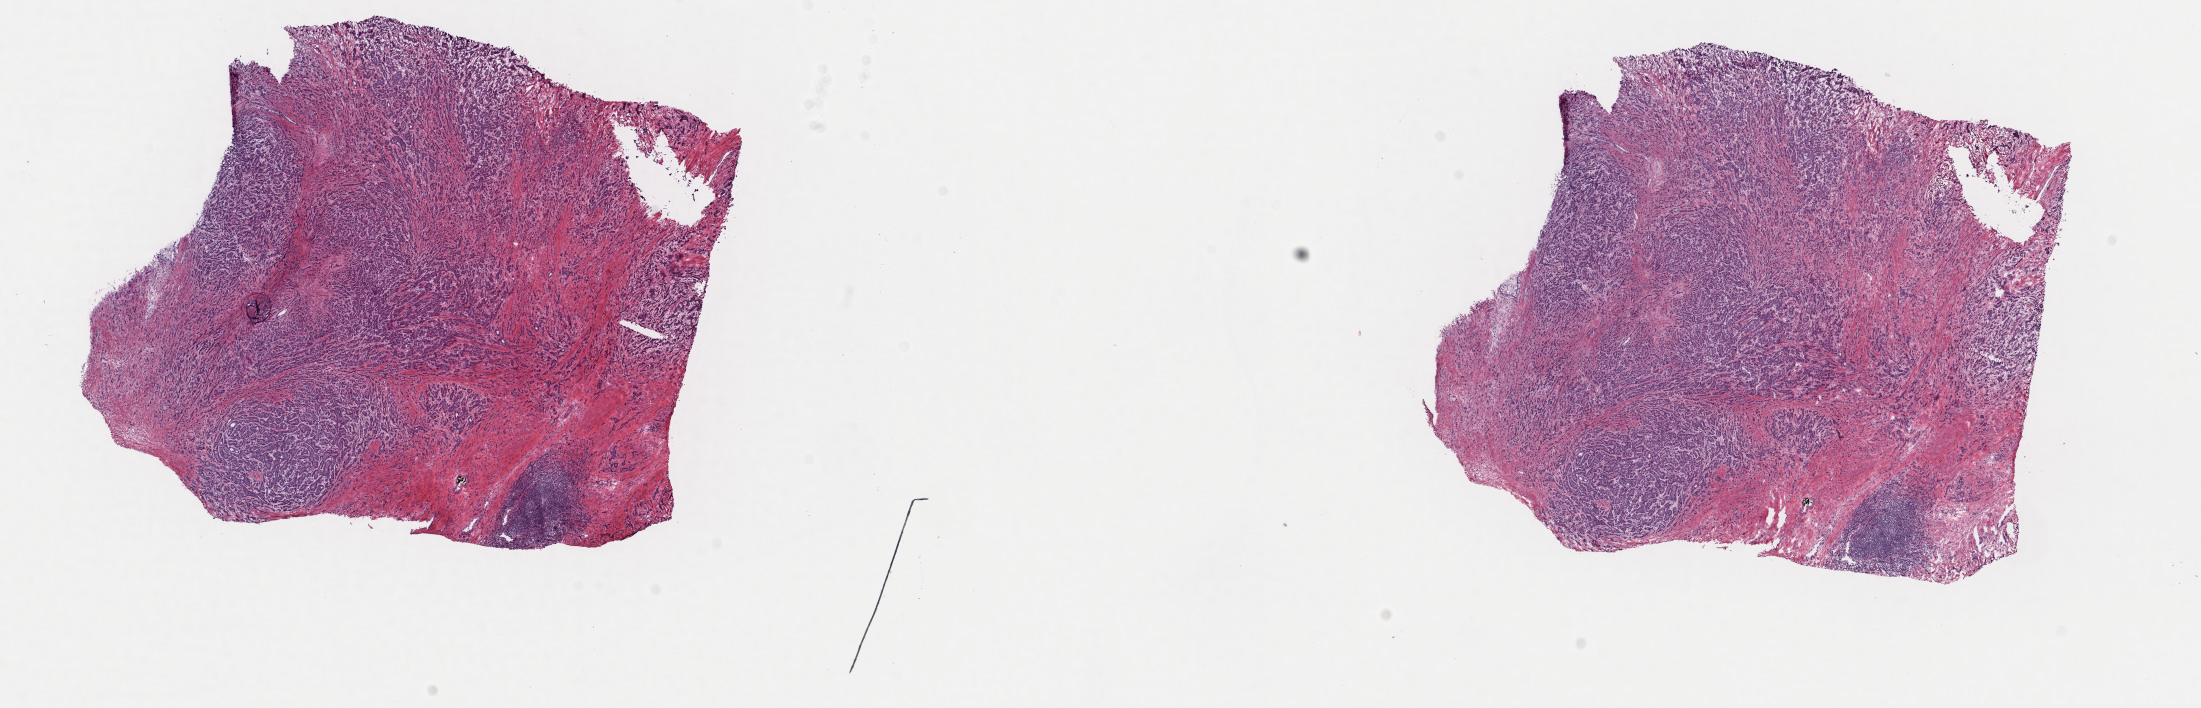
Whole-slide histology image, H&E-stained — low-resolution overview of the scanned area, about 17.4 x 5.6 mm (from a 40x scan); frozen section from the top of the tissue portion; sample: primary tumour, prostate. Patient: male, age at initial diagnosis 68 years. Gleason score: 9 (4+5). Slide review estimates, as recorded: tumour cells 70%, tumour nuclei 80%, normal cells 0%, stromal cells 30%, necrosis 0%. Inflammatory infiltration, as recorded: lymphocyte infiltration 100%, monocyte infiltration 0%, neutrophil infiltration 0%.
* lymph nodes positive (case pathology): 0 of 5 examined
* laterality: bilateral
* histologic diagnosis: Adenocarcinoma, NOS (prostate gland)